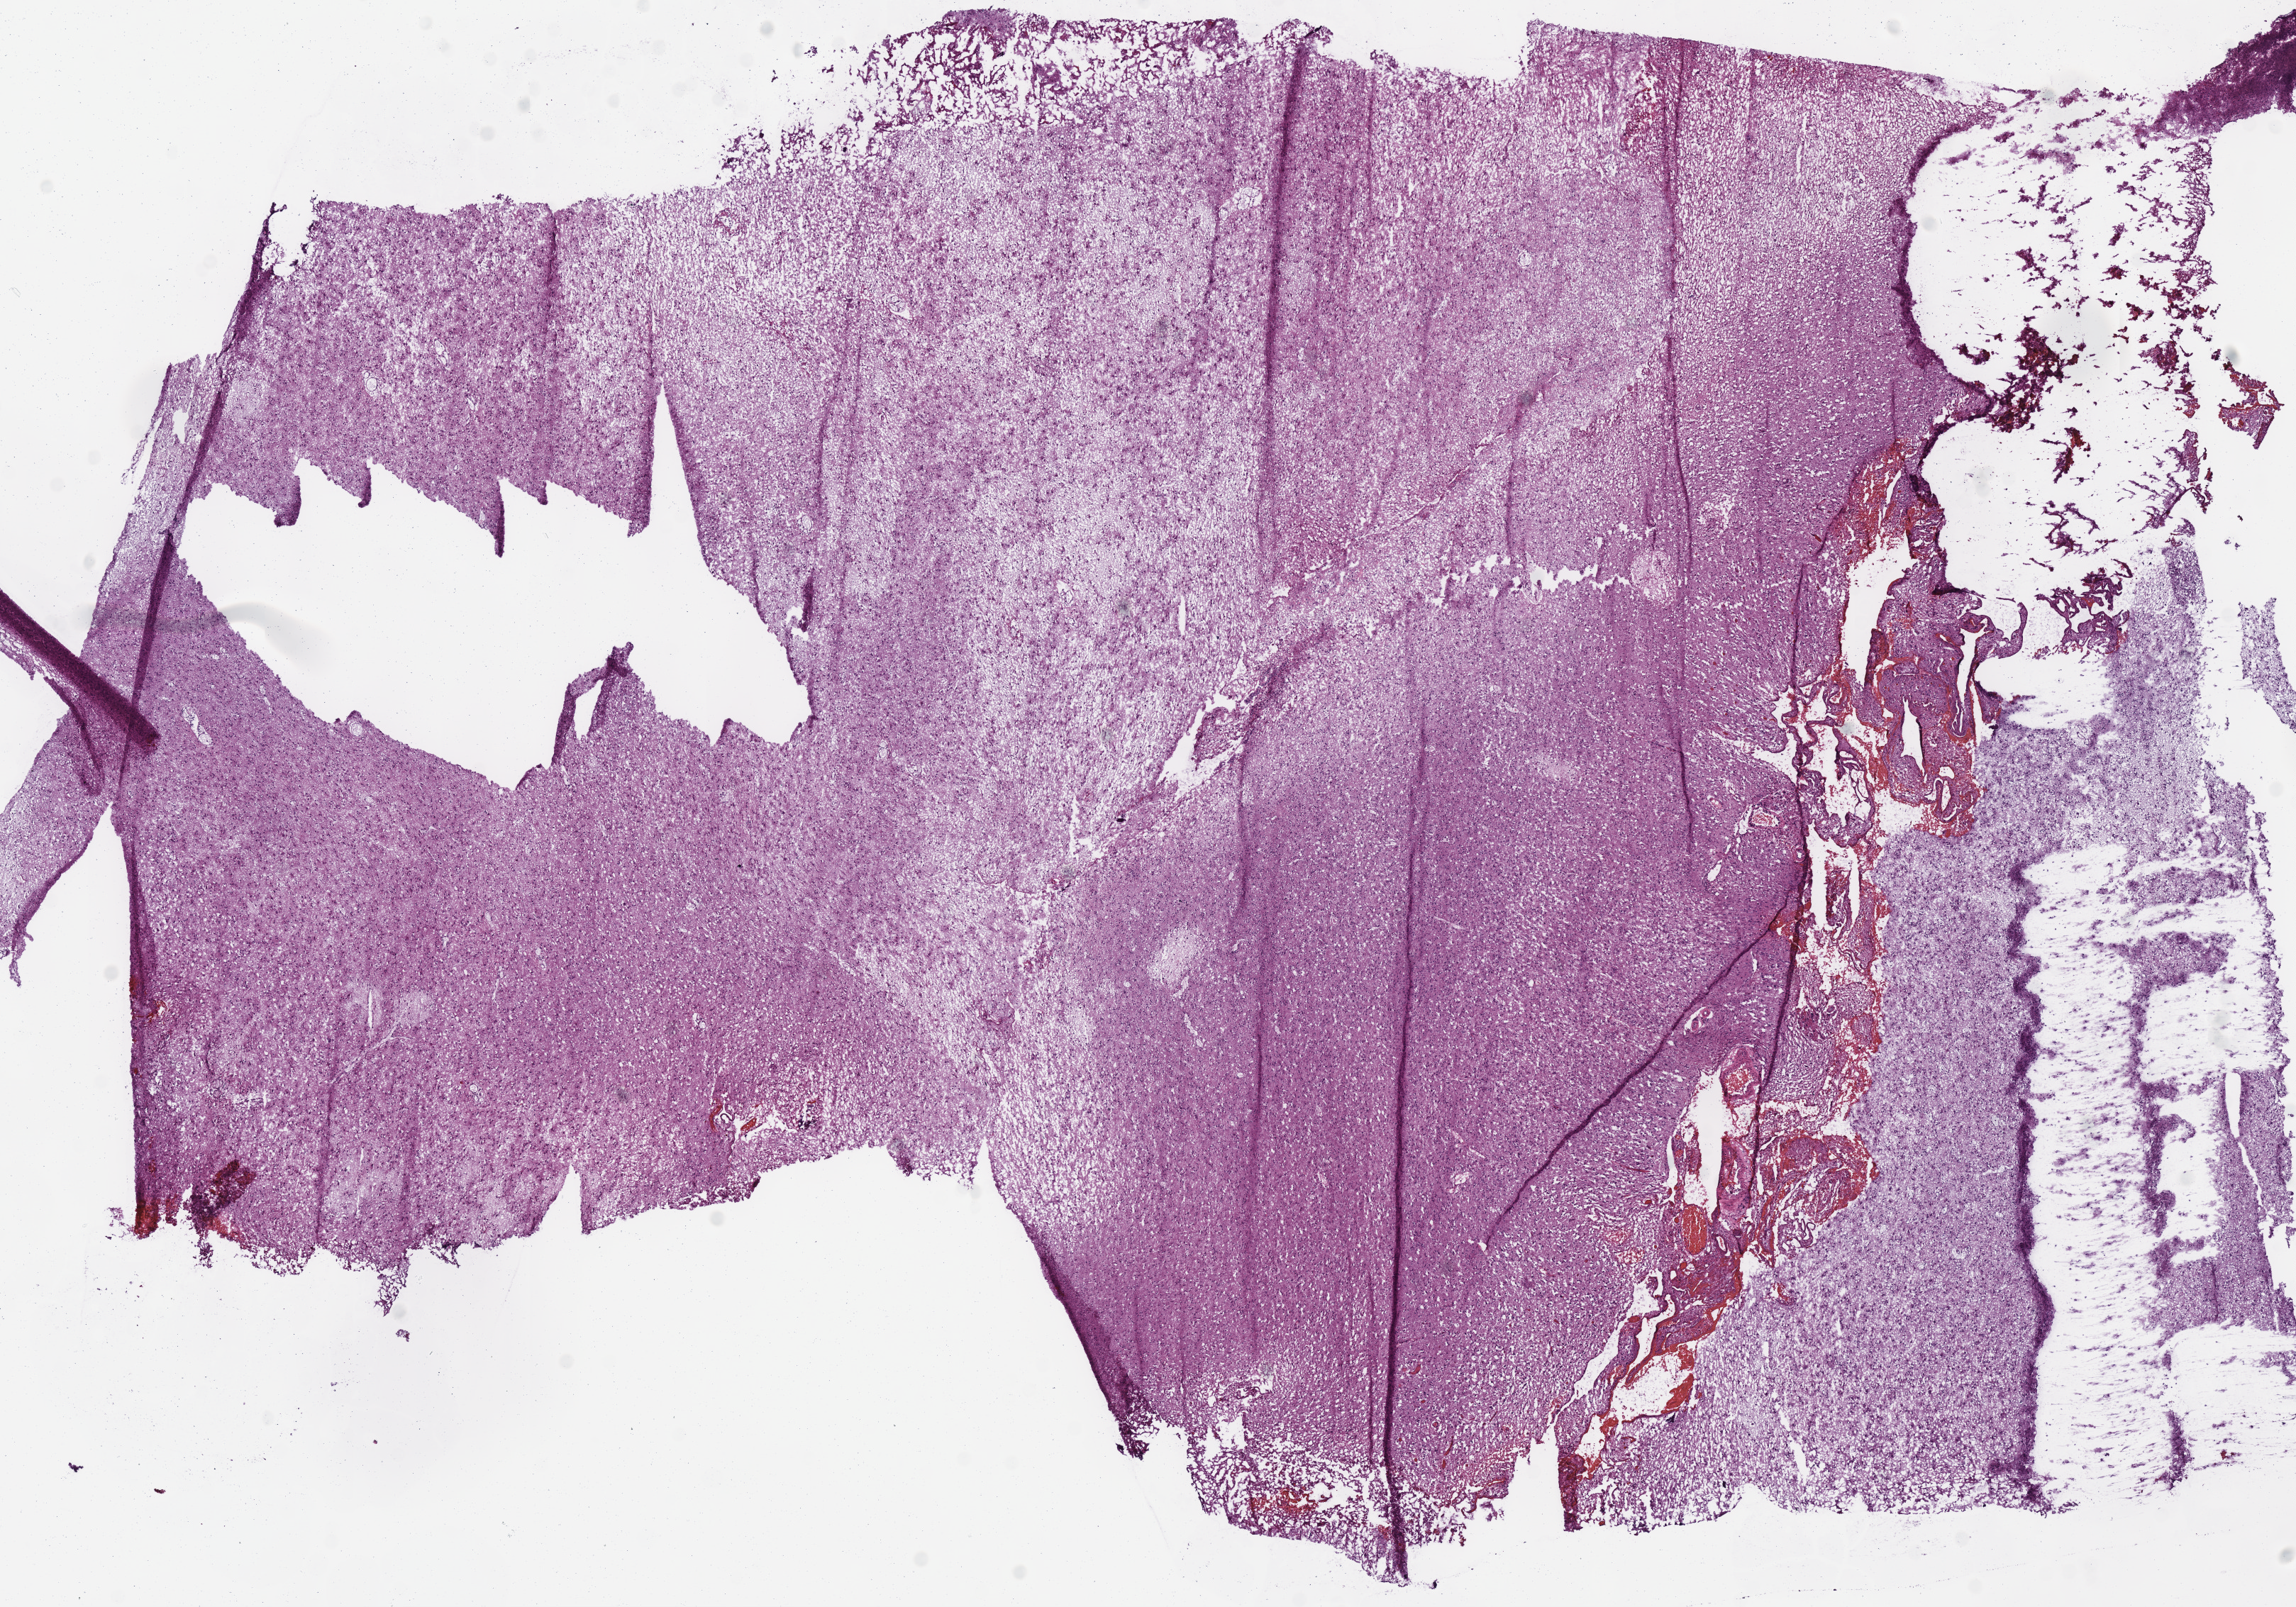
Whole-slide histology image, Hematoxylin and eosin (H&E) stained — low-resolution overview of the scanned area, about 12.7 x 8.9 mm, frozen section from the bottom of the tissue portion, primary tumour sample from the brain. Patient: male, age at initial diagnosis 57 years. Histologic grade: G3 (poorly differentiated). Composition of this section per pathologist review: tumour cells 100%, tumour nuclei 75%, normal cells 0%, stromal cells 0%, necrosis 0%.
- histologic diagnosis: Astrocytoma, anaplastic